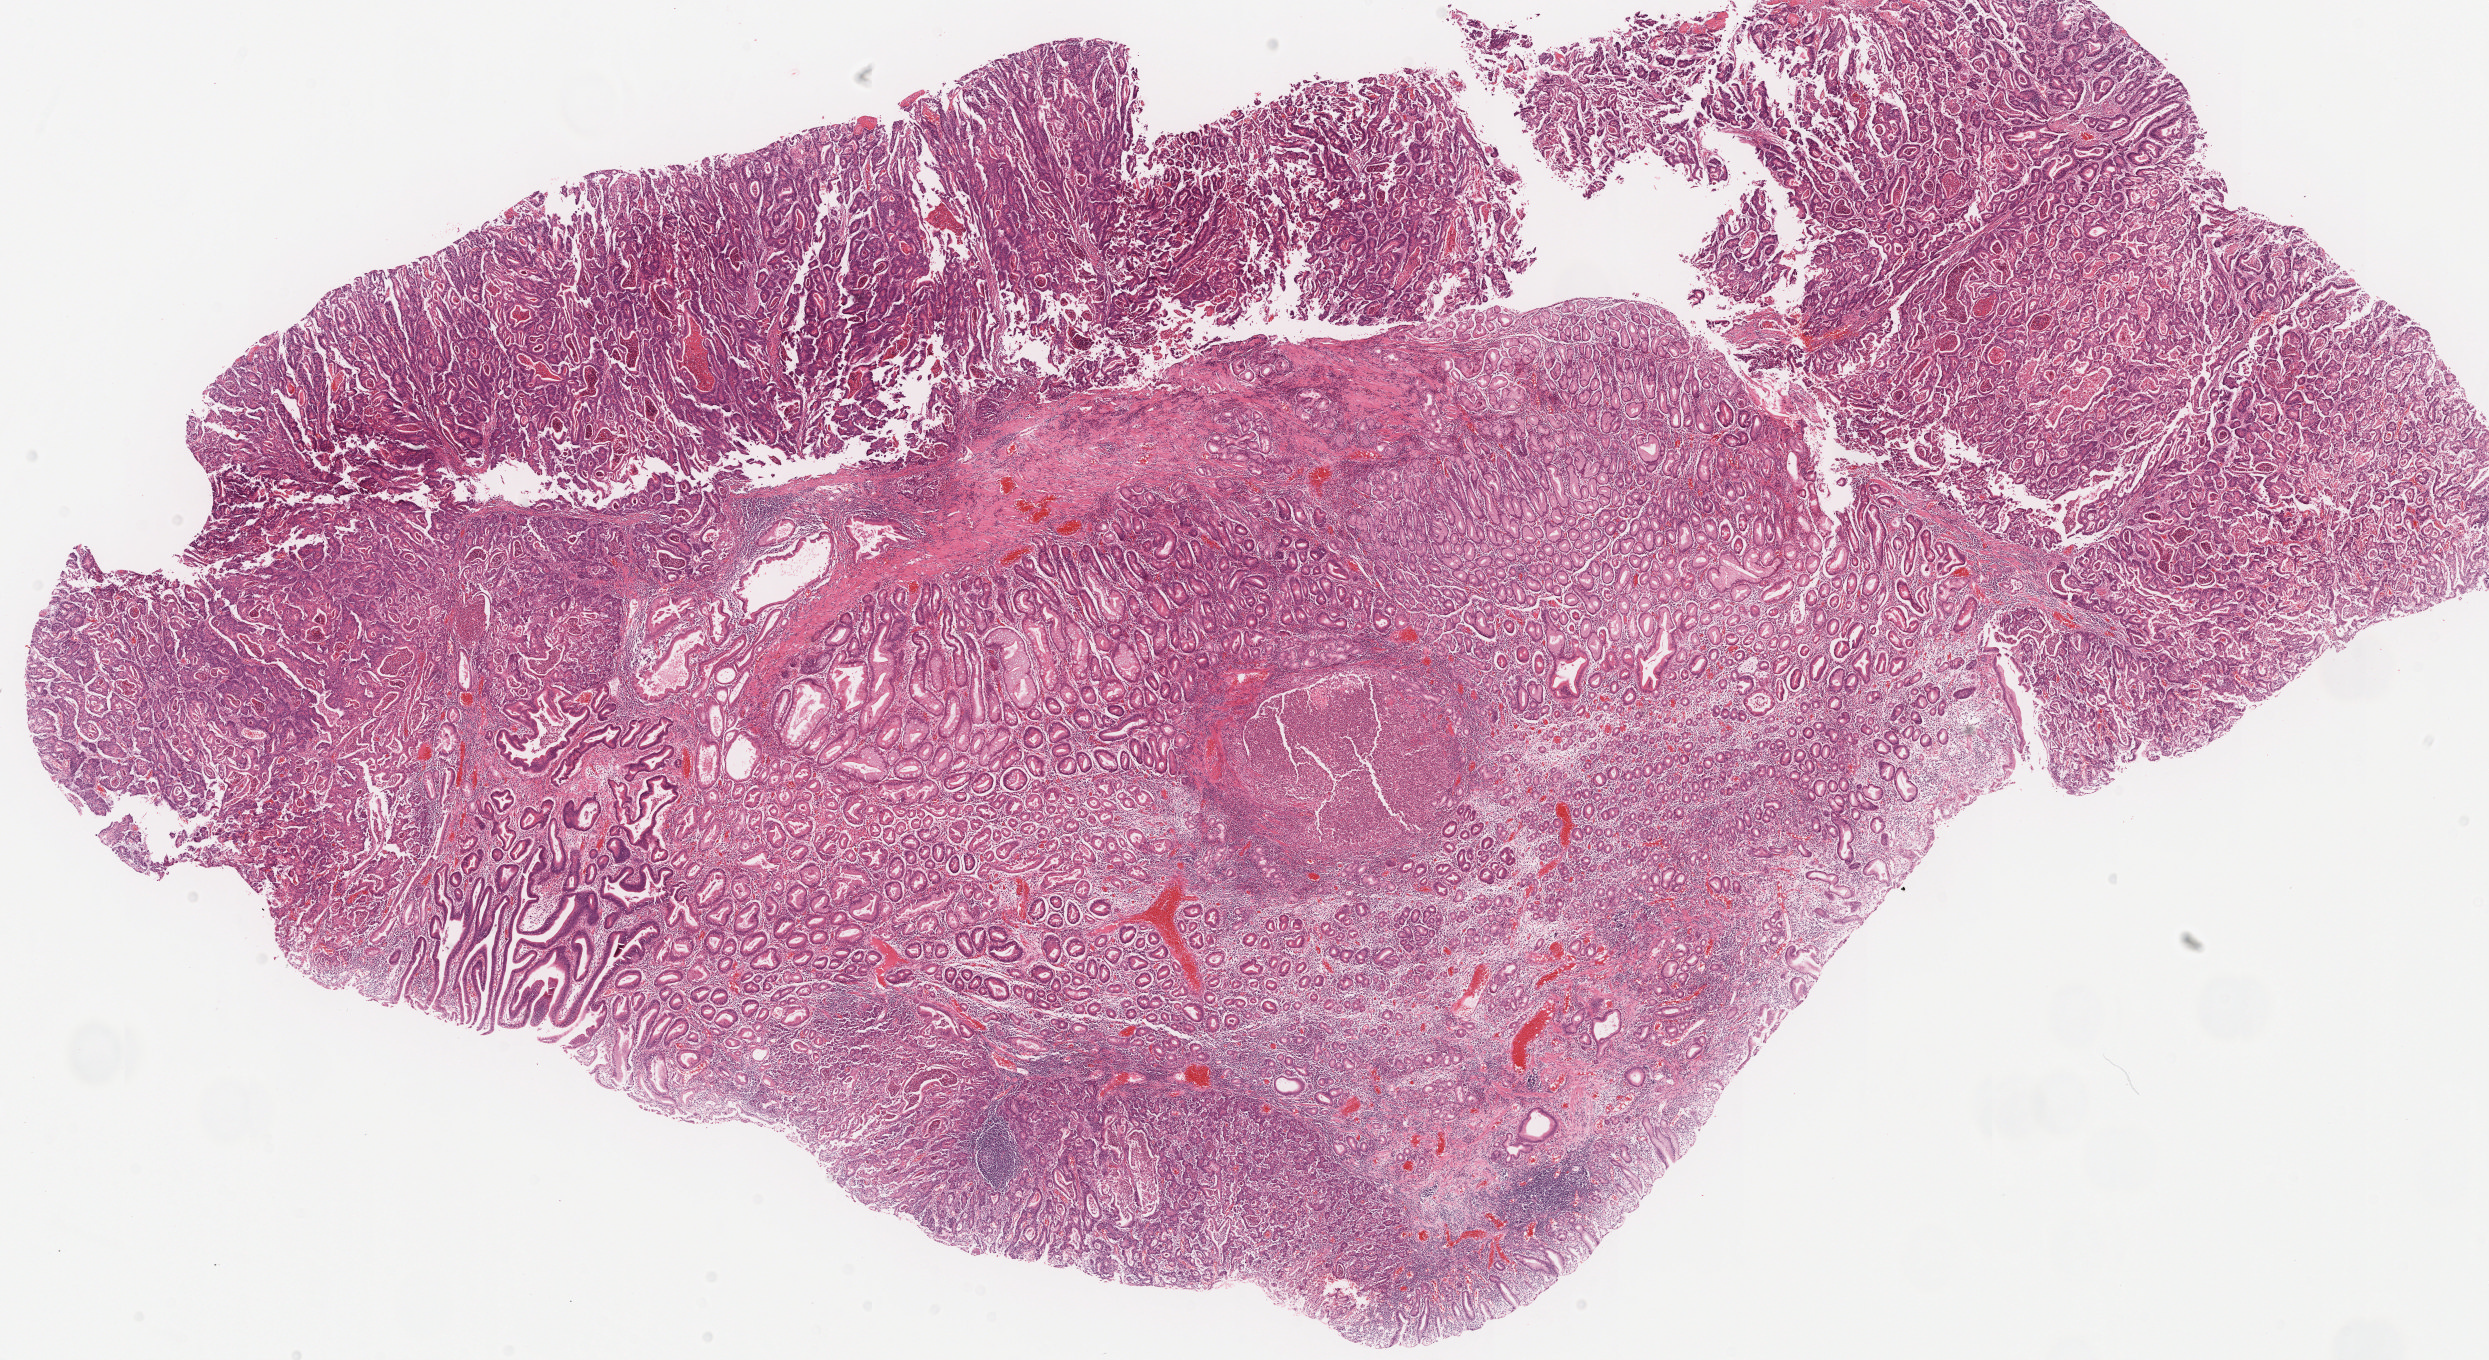
H&E whole-slide image — shown as a low-resolution overview of the whole scanned area (about 19.7 x 10.7 mm, acquisition: 20x scan). Formalin-fixed paraffin-embedded (FFPE) diagnostic section. Stomach, primary tumour sample. Female, age 71 years at initial diagnosis. Histologic grade: G3 (poorly differentiated).
• lymph nodes positive (case pathology): 0 of 81 examined
• pathologic diagnosis: Tubular adenocarcinoma (gastric antrum)
• AJCC pathologic stage: IIA (7th edition)